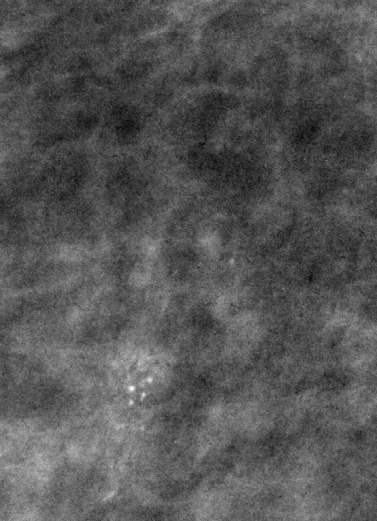
Region of interest cut from a scanned film mammogram (one marked finding), right breast, MLO view.
Calcifications, morphology pleomorphic, distribution clustered; BI-RADS assessment category 4; subtlety rating 3 on a 1 (subtle) to 5 (obvious) scale; pathology result (as recorded, not read from the image): malignant.